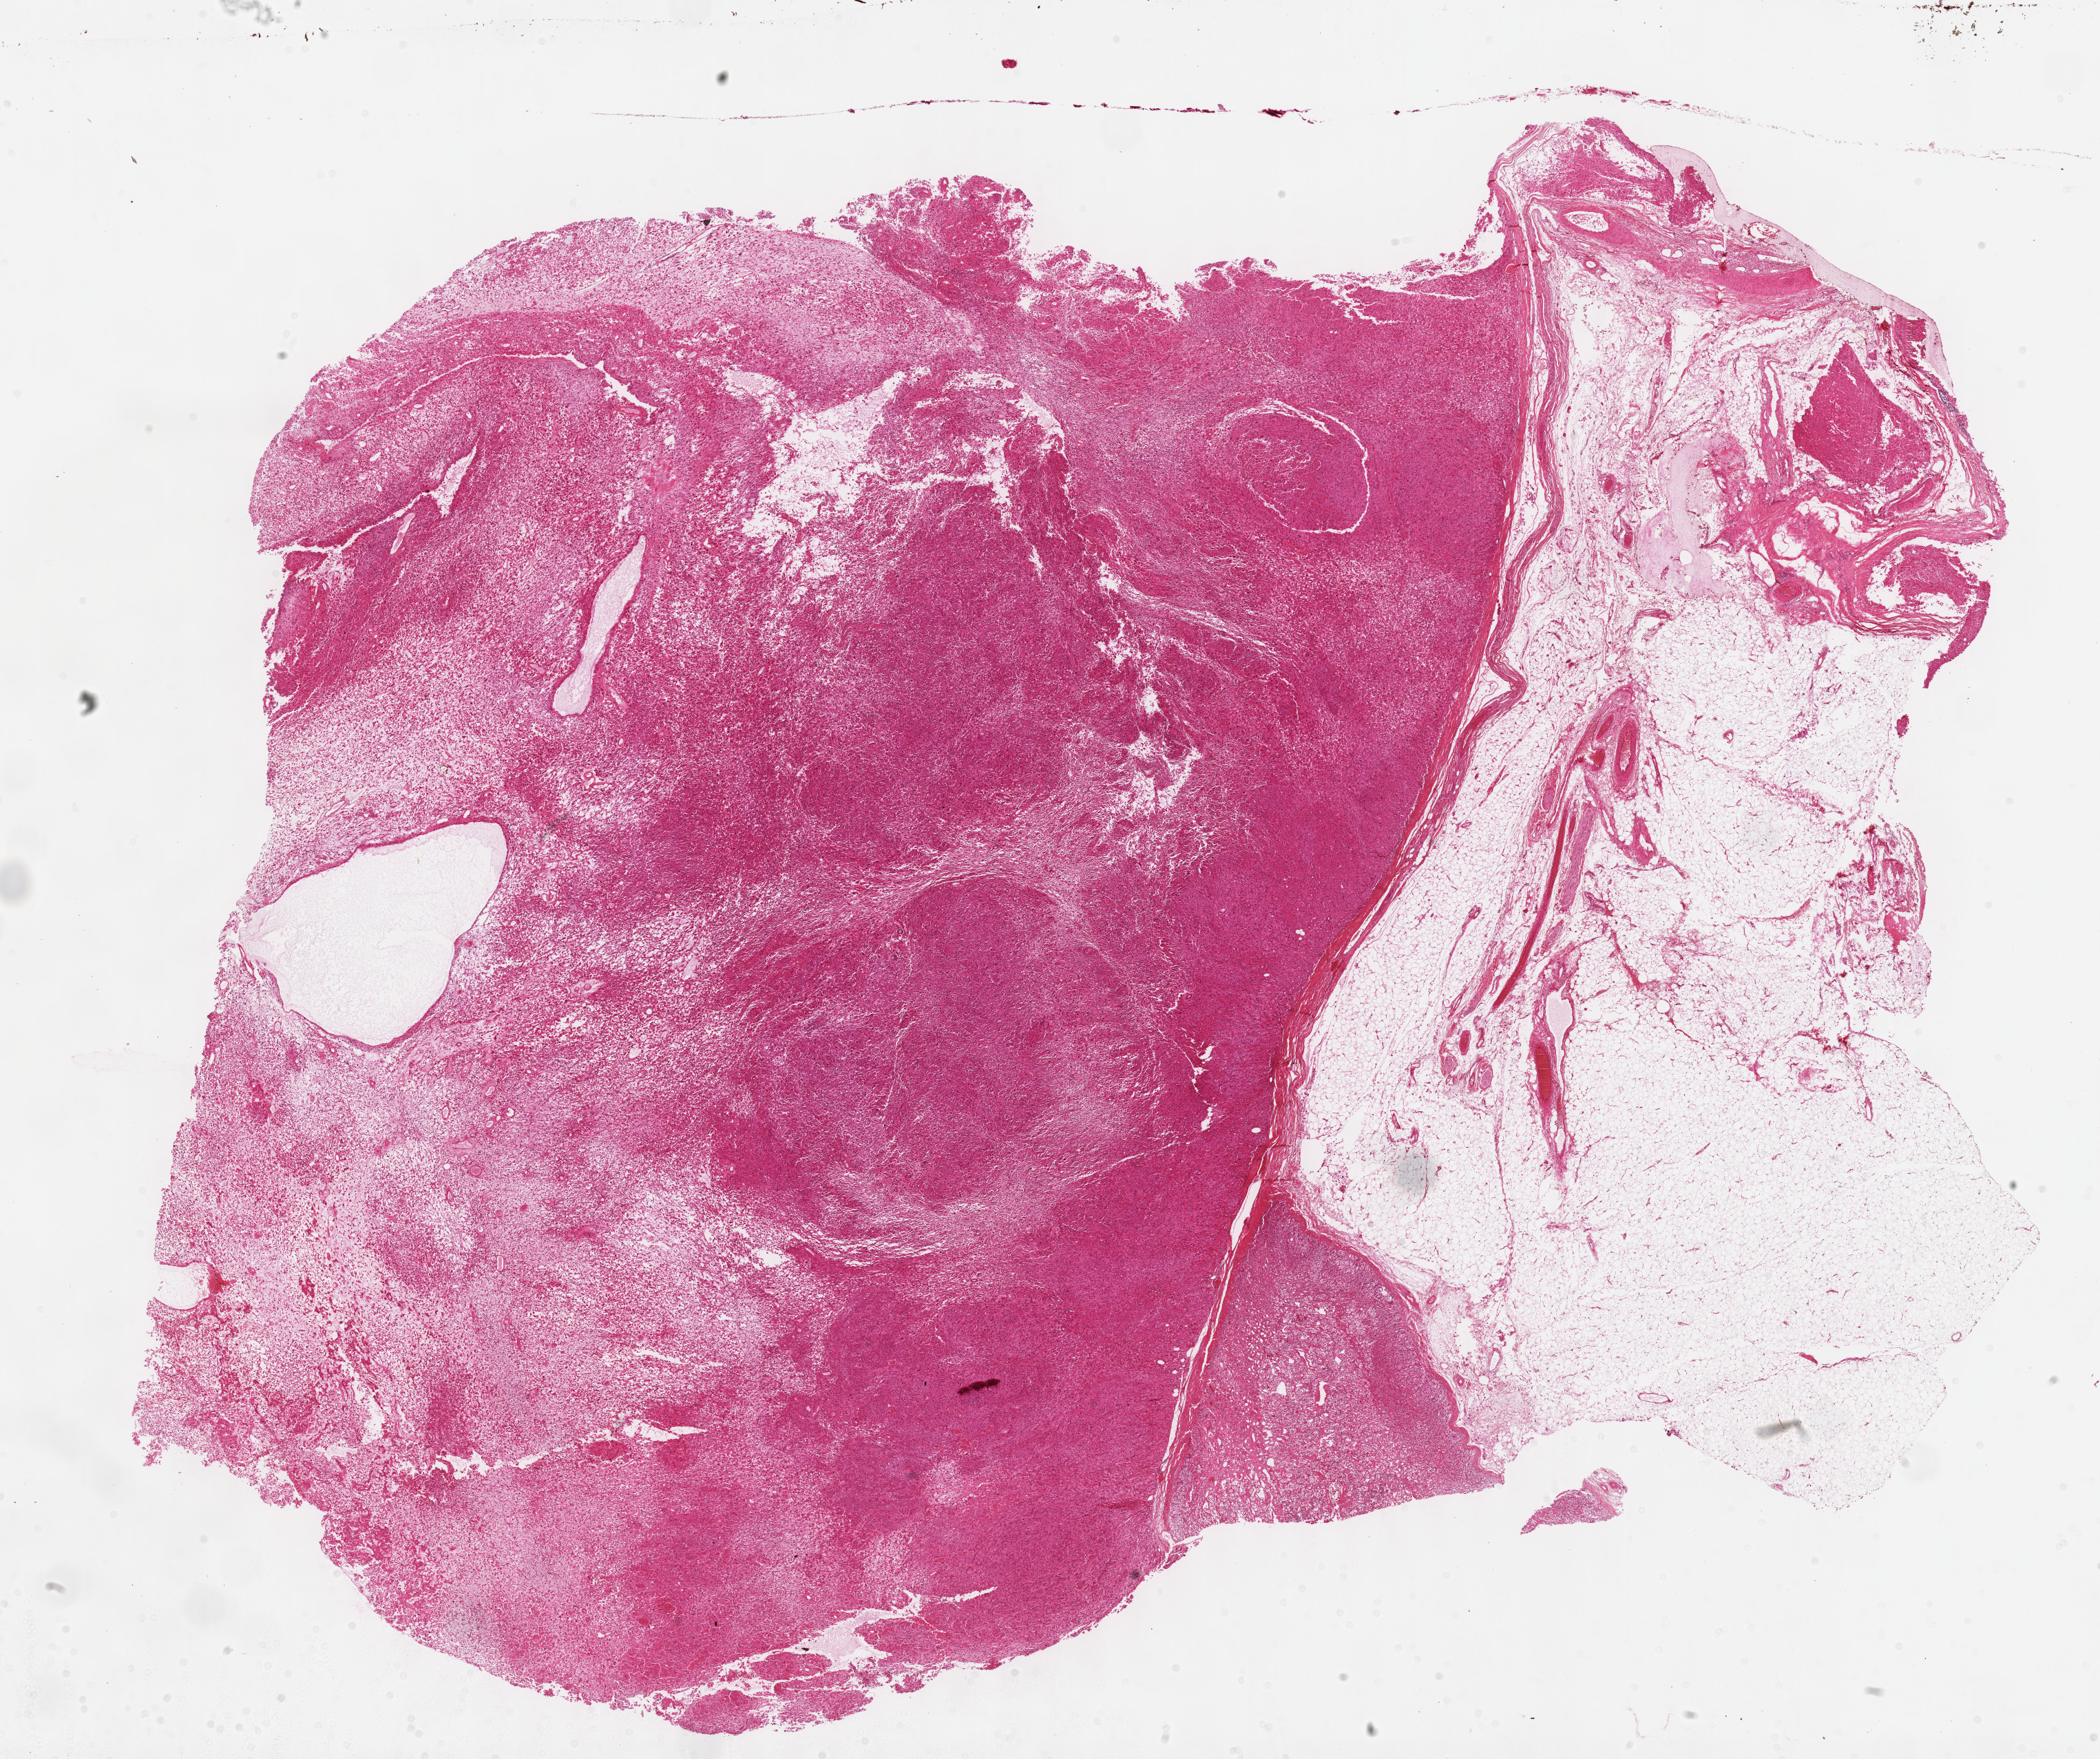
Whole-slide histology image, H&E — low-resolution overview of the scanned area, about 24.6 x 20.6 mm (acquisition: 40x scan). Formalin-fixed paraffin-embedded (FFPE) diagnostic section. Sample: primary tumour, adrenal cortex. Male, age 57 years at initial diagnosis.
• laterality: left
• diagnosis: Adrenal cortical carcinoma (cortex of adrenal gland)